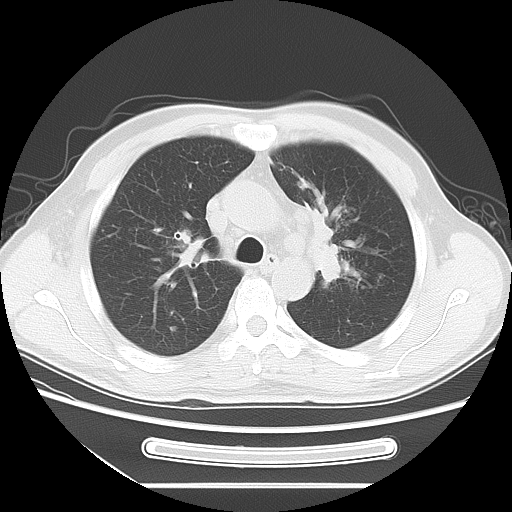
Chest CT, one axial slice. Position 50 of 71 along the scan axis. Lung window (W 1500 / L -600 HU). 5 mm slice thickness. 512 × 512 image matrix, field of view 366 × 366 mm. Patient: male, 51 years. From the clinical record (not read from this slice): clinical TNM (as recorded): T1c N3 M0.
Annotated regions visible in this slice (rectangle marked by the reading radiologist):
- lung tumour (recorded histology: adenocarcinoma): bounding box <301,192,360,289> (left, top, right, bottom; pixels)